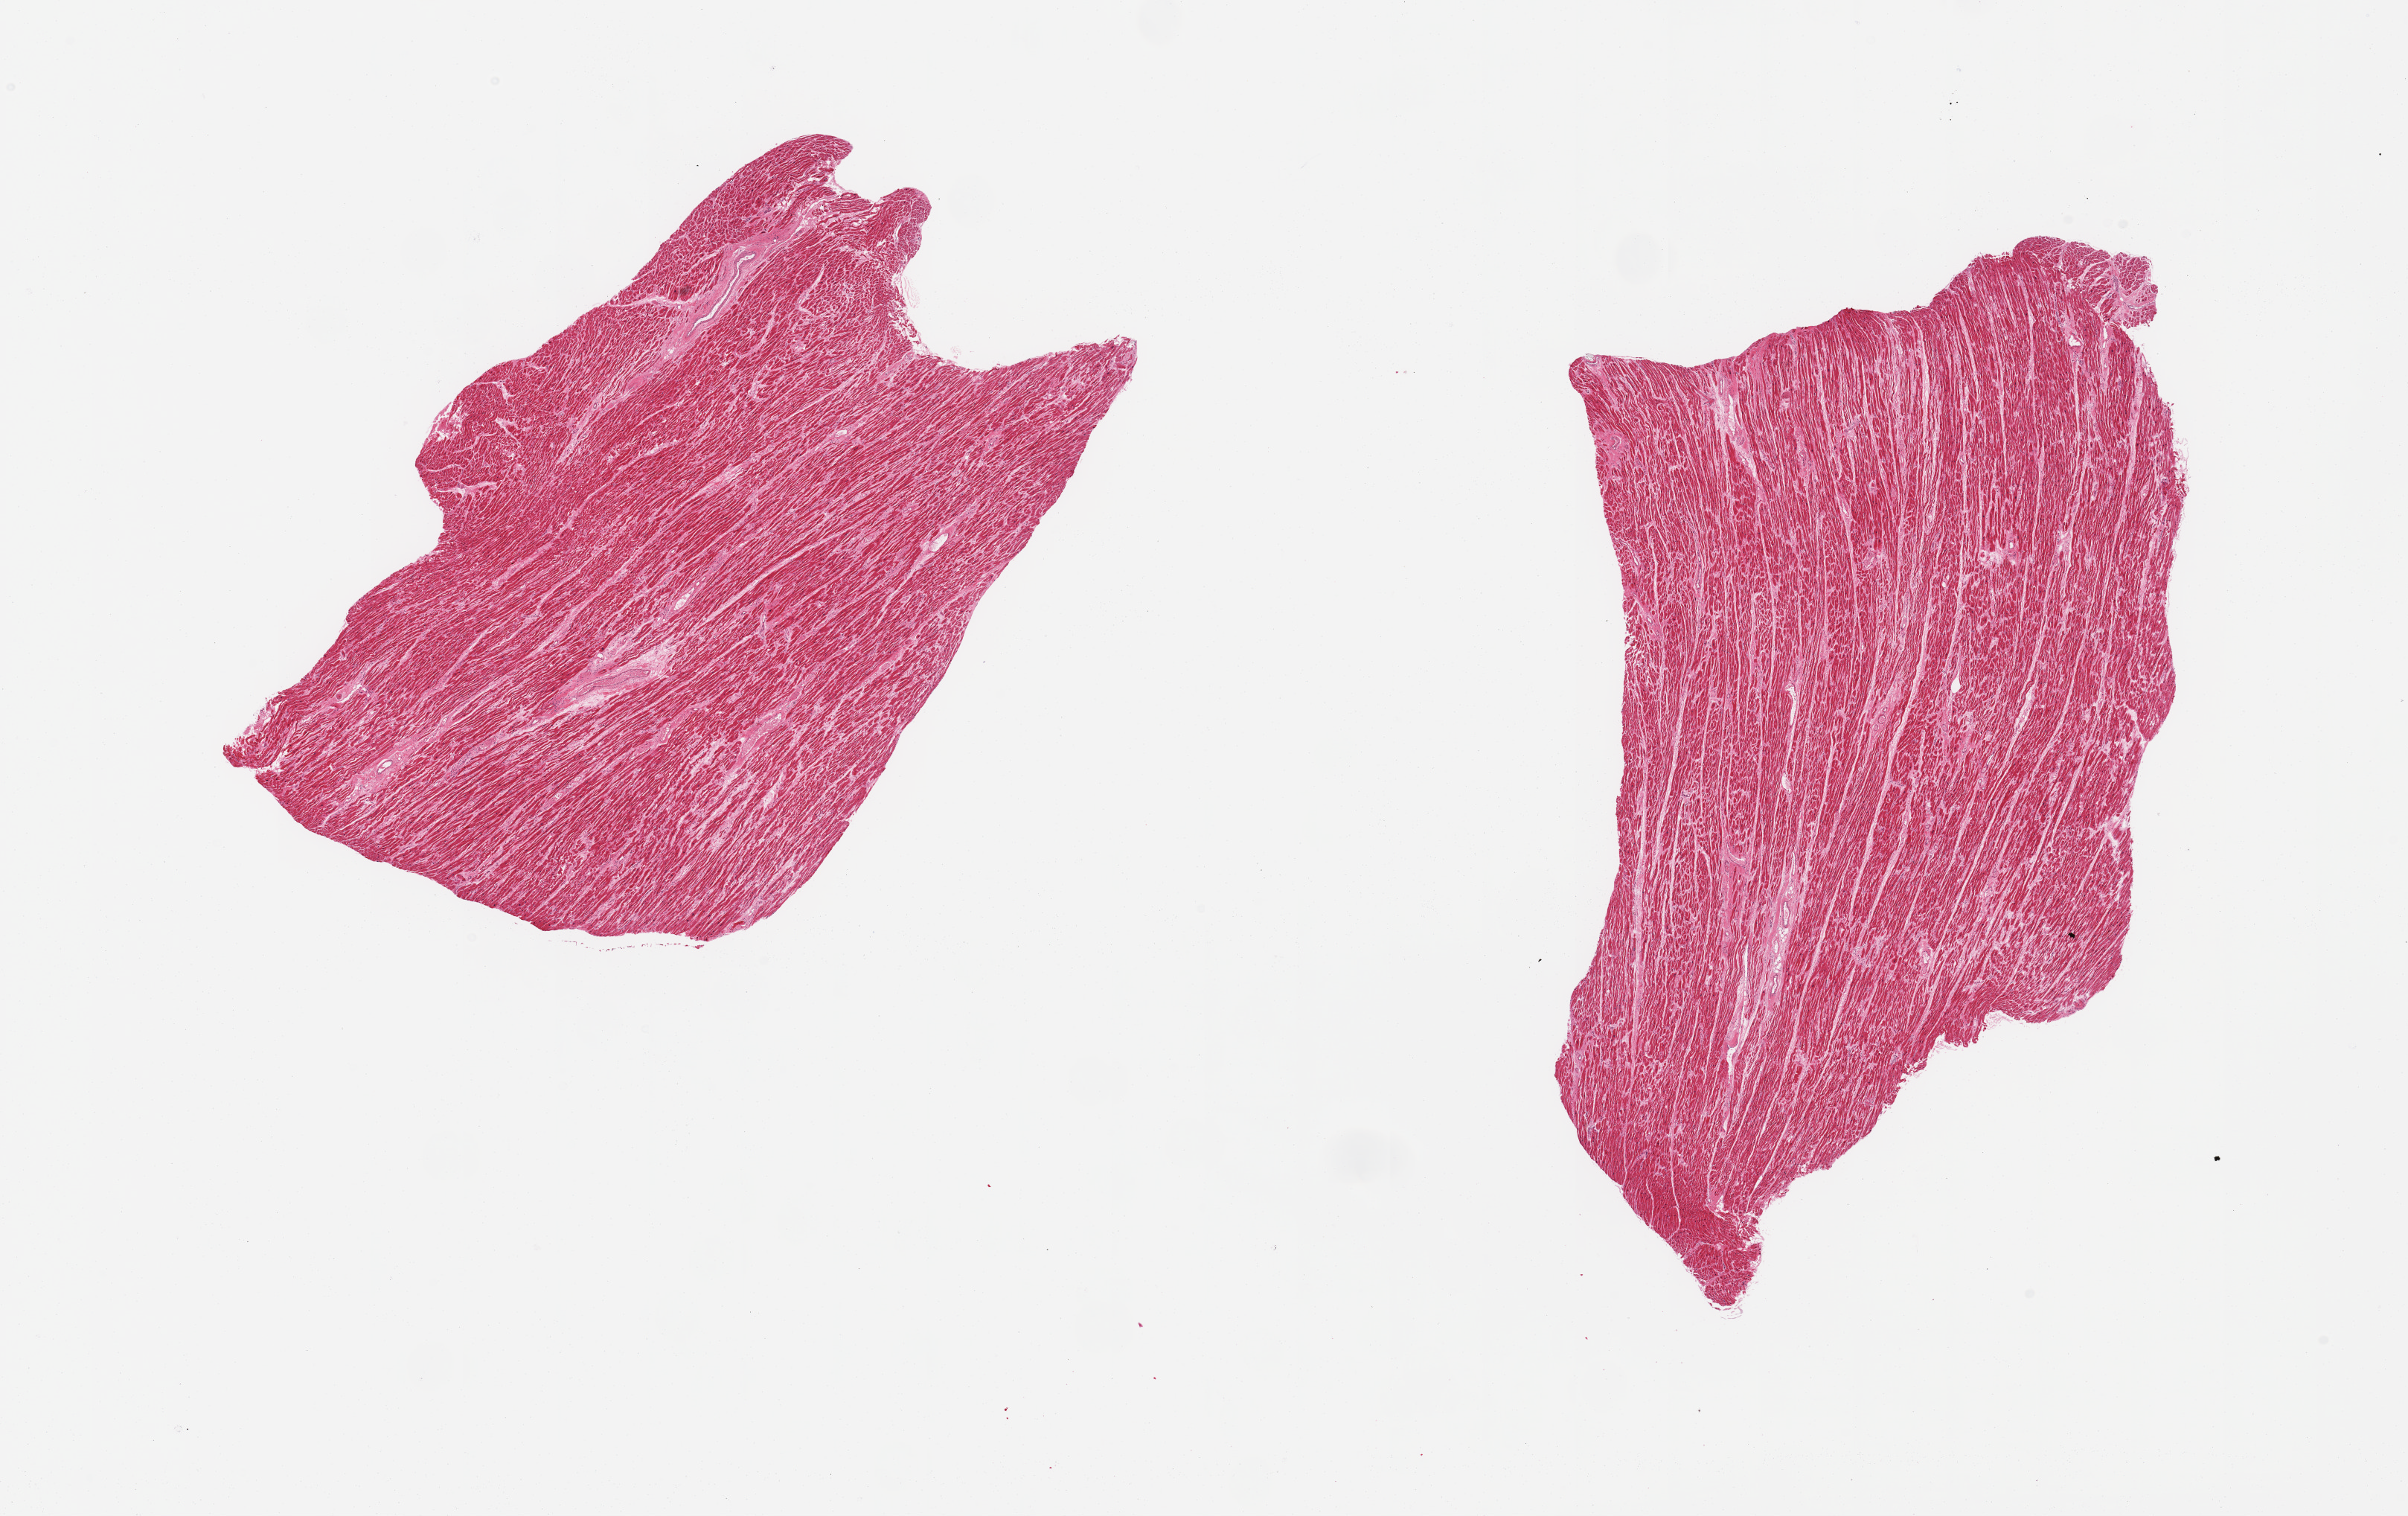
Whole-slide image, hematoxylin and eosin (H&E) stain, brightfield — a low-resolution overview of the entire scanned area, about 25.6 x 16.1 mm (acquisition: 20x scan). PAXgene-fixed paraffin-embedded (PFPE) section. Section of heart (target tissue). Donor tissue sample. Donor: male.
* reviewer comment on this tissue sample: 2 pieces; interstitial fibrosis